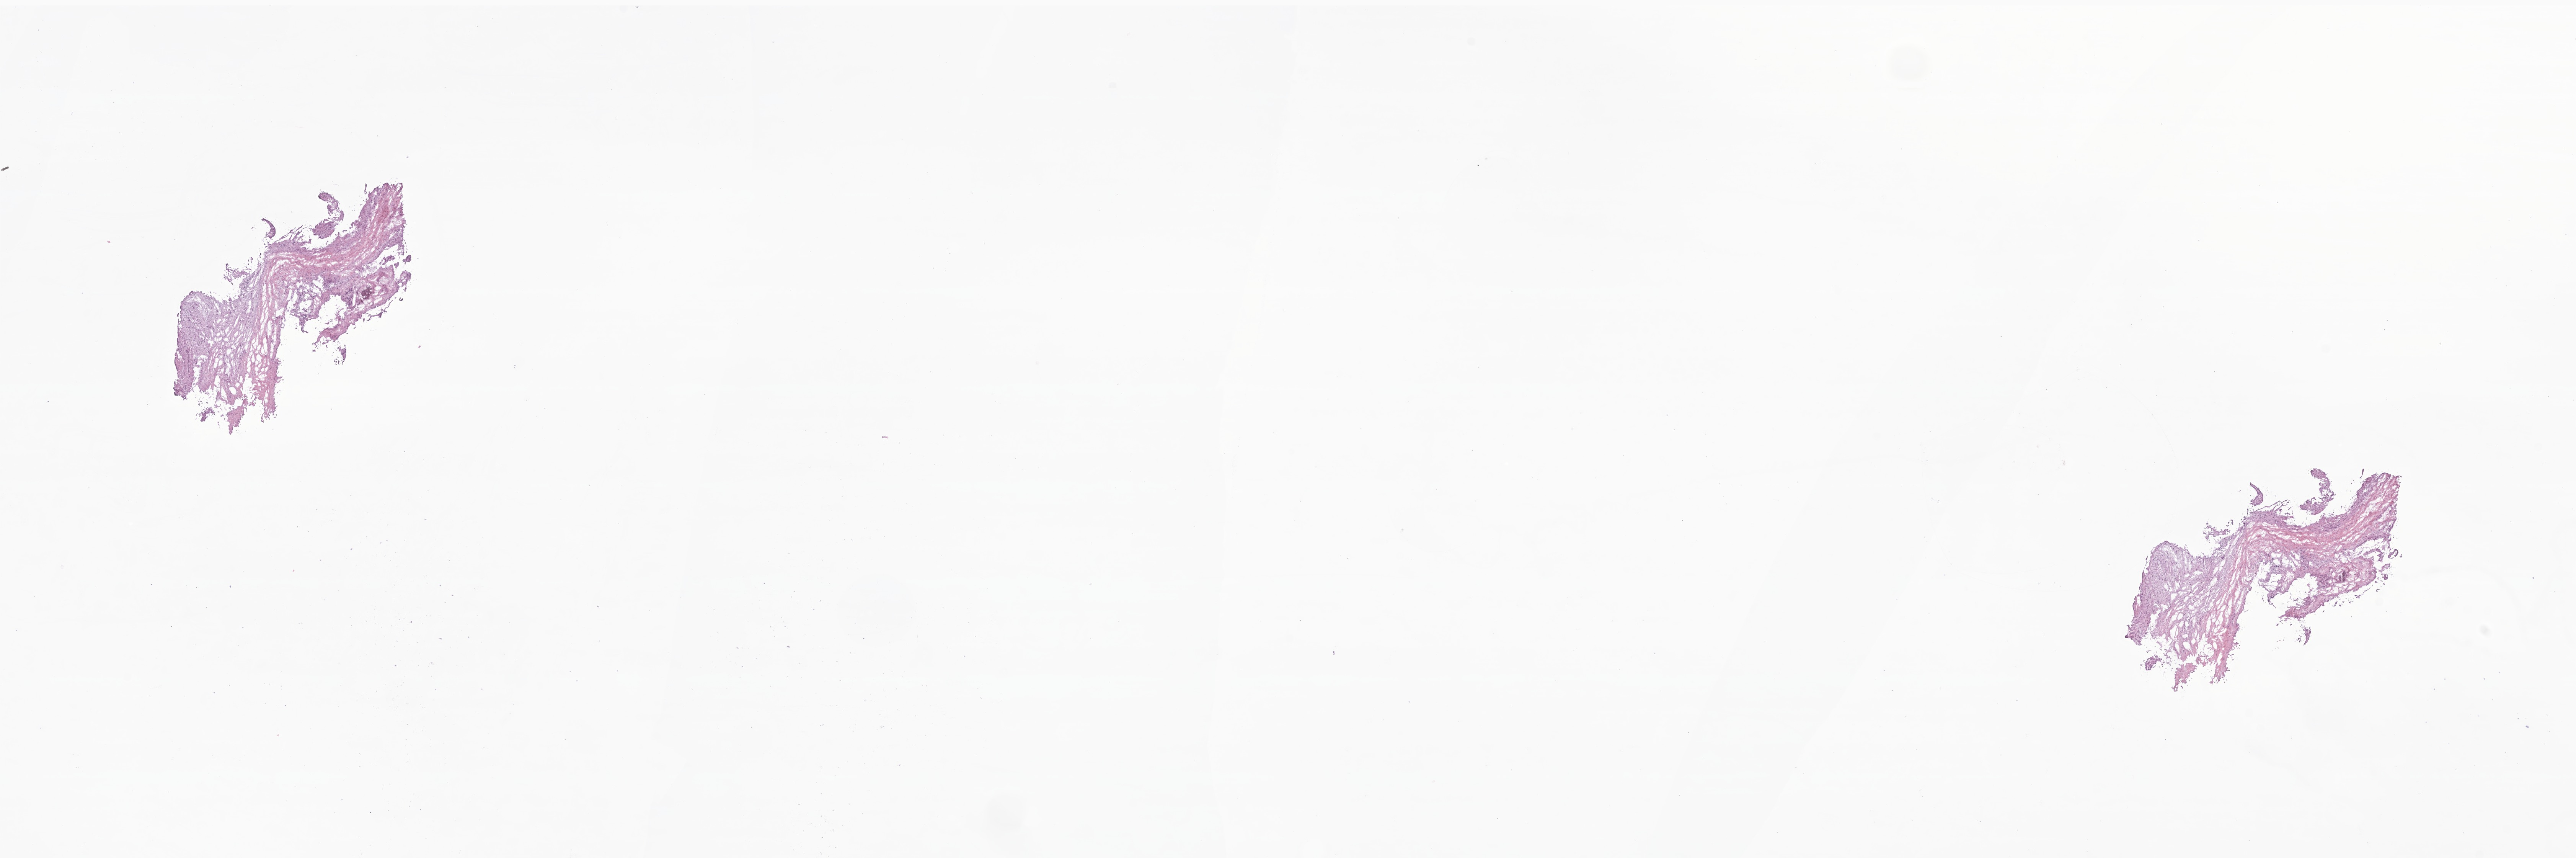
Whole-slide image, H&E stain of tumor tissue from the adrenal gland, low-resolution overview of the scanned area, about 28.4 x 9.4 mm. Cryosection (OCT / tissue freezing medium). Patient: male, age 42 months (3 years 6 months).
Diagnosis (ICD-O-3 morphology term): Neuroblastoma, NOS.